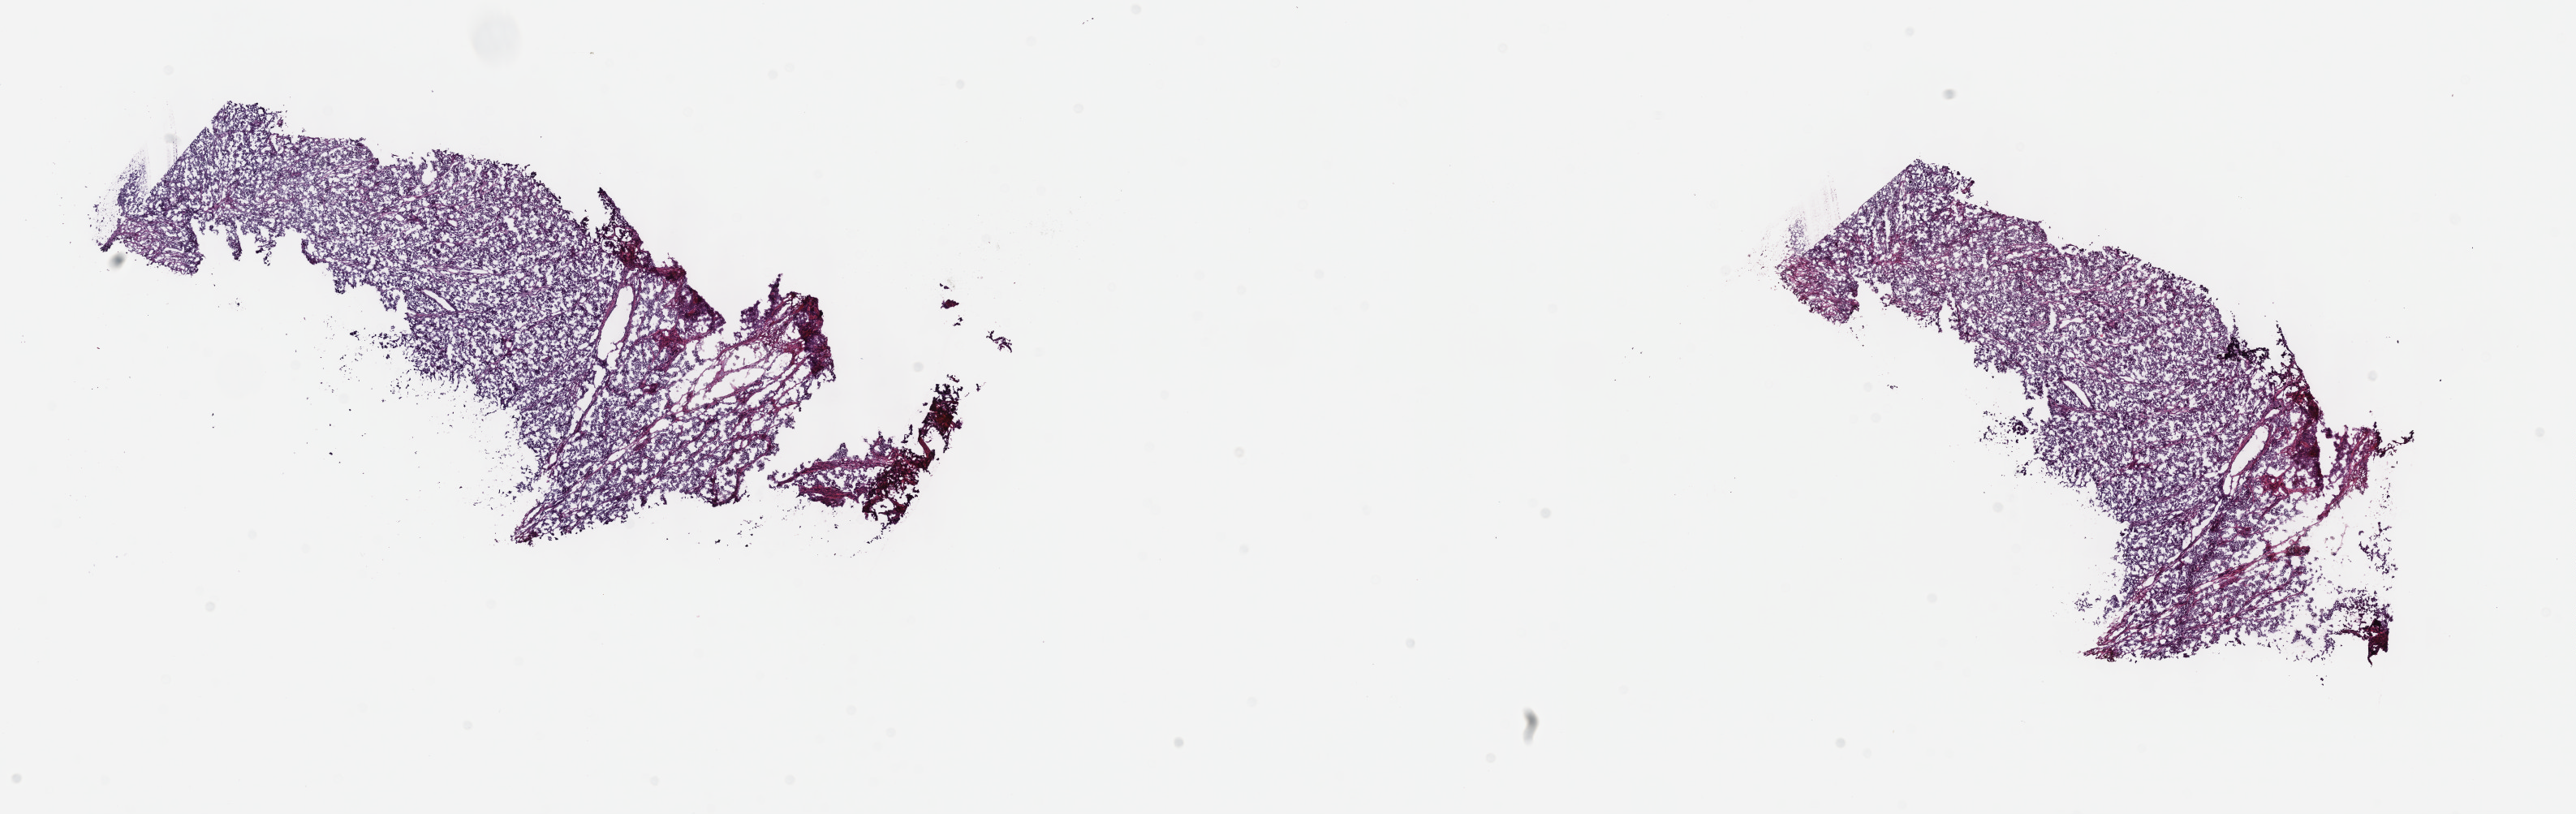
H&E-stained whole-slide image, whole scanned area (about 25.7 x 8.1 mm, acquisition: 40x scan) shown as a low-resolution overview. Frozen section. Sample: primary tumour, skin. Male patient; age at initial diagnosis 66 years. Pathologist review of this section (percent, as recorded): tumour cells 100%, tumour nuclei 75%, normal cells 0%, stromal cells 0%, necrosis 0%. Inflammatory infiltration, as recorded: lymphocyte infiltration 2%, monocyte infiltration 0%, neutrophil infiltration 0%.
TNM: T4b N0 M0. AJCC pathologic stage: IIC (7th edition). Pathologic diagnosis: Malignant melanoma, NOS.